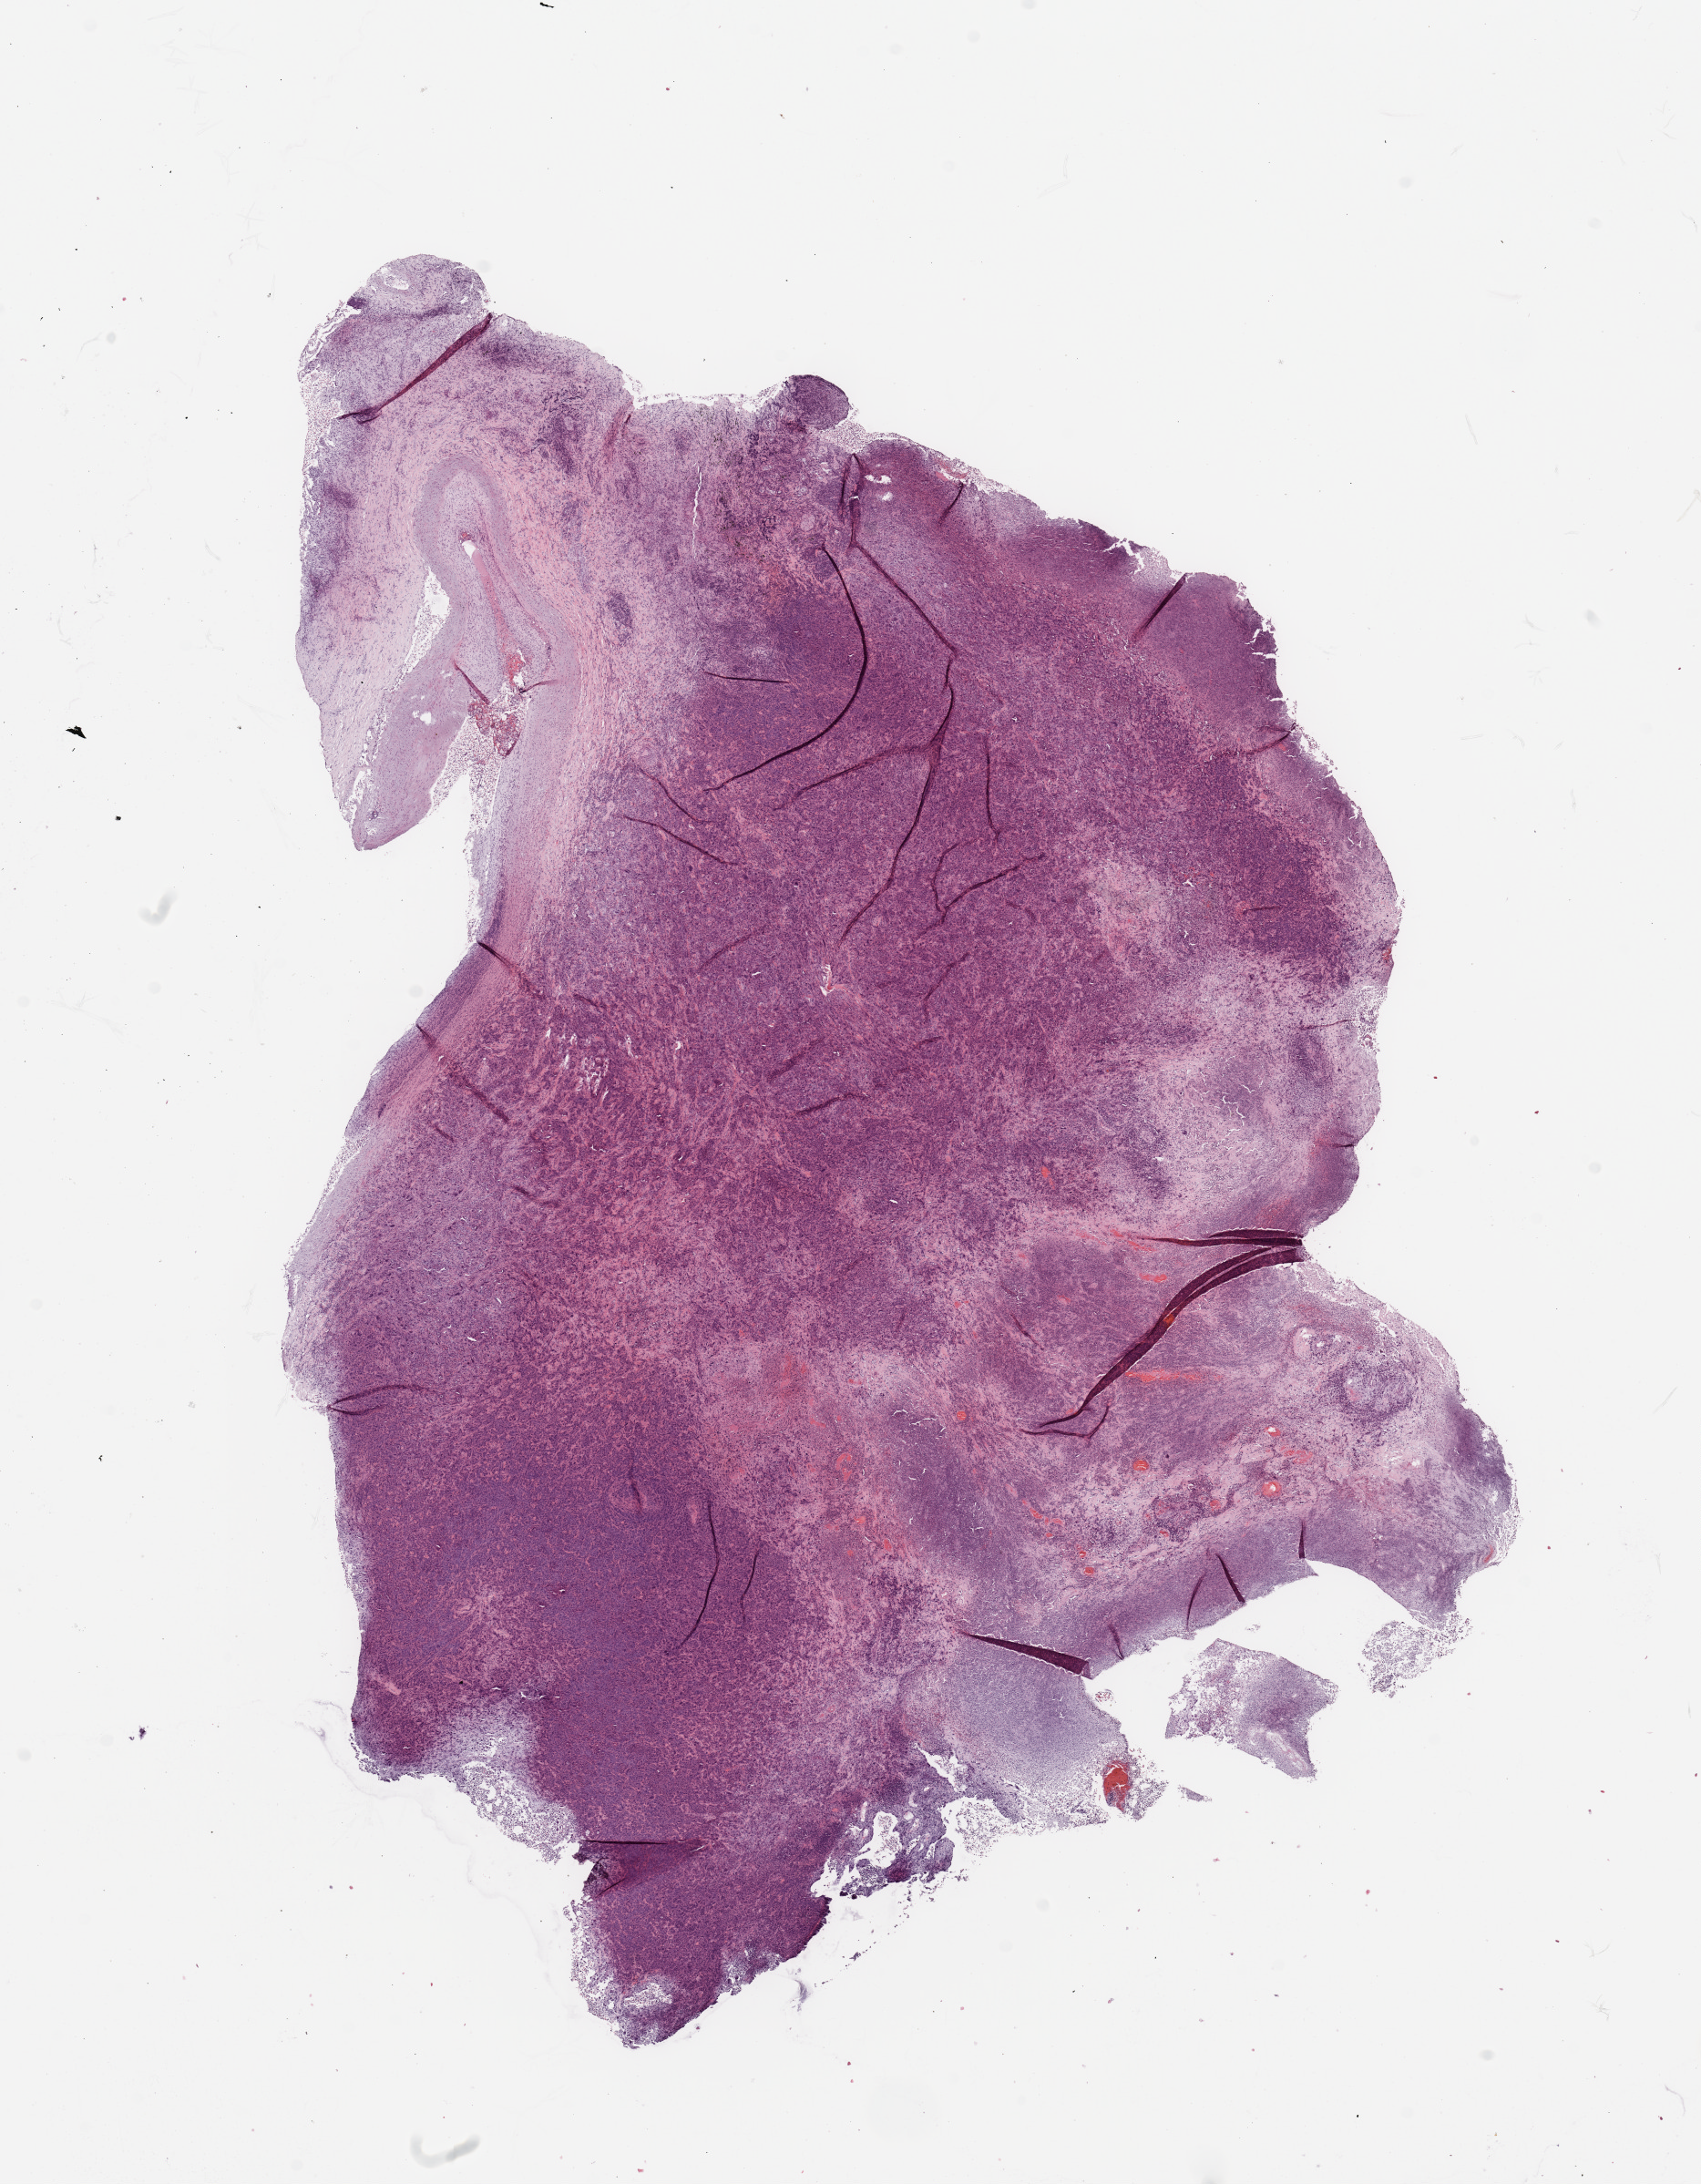
Digitized H&E tissue section (whole slide), a low-resolution overview of the entire scanned area, about 14.8 x 19.0 mm (from a 20x scan). Tumour tissue sample, lung. Patient: female, age 70 years. Histologic grade: G3 (poorly differentiated).
* primary tumour site (as recorded): right lower lobe
* diagnosis: Squamous cell carcinoma, NOS